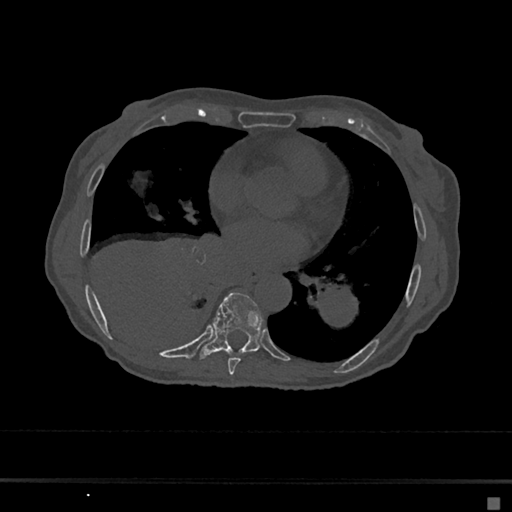
CT including the spine, one axial slice. Position 342 of 797 along the scan axis. Reconstruction kernel Br40s/3. Bone window (W 1800 / L 400 HU). 0.5 mm slice thickness. 512 × 512 image matrix, field of view 360 × 360 mm. Patient: female, 68 years. Case-level facts recorded for this patient, not image findings: primary cancer: renal.
Annotated regions visible in this slice (semi-automatically segmented with operator editing):
- T7 vertebra: box from (x=228, y=358) to (x=241, y=375) px
- T8 vertebra: (x=199, y=292)–(x=262, y=359)